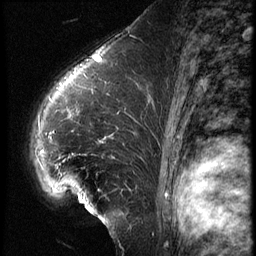
Breast MRI (dynamic contrast-enhanced), one sagittal slice. Position 42 of 62 along the scan axis. 3 images stored at this slice position (order not interpretable as contrast timing). 1.5 T. TE 4.2 ms, TR 9 ms. 2.5 mm slice thickness. 256 × 256 image matrix. Female patient, age 39 years. Case-level facts recorded for this patient, not image findings: setting: breast cancer imaged before/during neoadjuvant chemotherapy; receptor status: HER2-positive.
Structures marked on this image (semi-automatic segmentation, software-assisted and operator-edited):
- analysis volume of interest (the breast-tissue region the enhancement analysis was run in; not a lesion): box from (x=25, y=64) to (x=153, y=228) px
- tumour enhancement mask (voxels above the 140 % enhancement threshold inside the analysis volume of interest): (x=53, y=79)–(x=114, y=138)